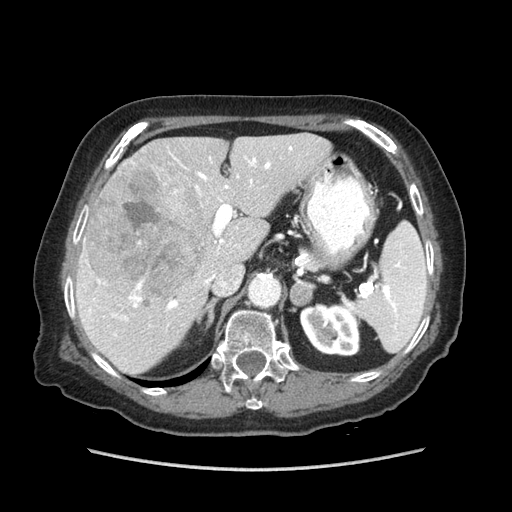
Contrast-enhanced abdominal CT (liver protocol), one axial slice. Slice 49 of 89 in the series (ordered by position). Reconstruction kernel STANDARD. 140 kVp. Soft-tissue window (W 400 / L 40 HU). 2.5 mm slice thickness. 512 × 512 image matrix, field of view 360 × 360 mm. From the clinical record (not read from this slice): diagnosis: hepatocellular carcinoma (patient treated with transarterial chemoembolisation; whether this scan precedes or follows treatment is not stated here); TNM stage (as recorded): Stage-IIIA; Child-Pugh class: A; tumour nodularity: multinodular; tumour size: 11 cm.
Structures marked on this image (semi-automatic segmentation, software-assisted and operator-edited):
- liver parenchyma outside the tumour (the mass and vessels are separate outlines, so this box may not span the whole liver): bounding box <76,134,330,374> (left, top, right, bottom; pixels)
- mass: <84,159,207,298>
- liver vessels: <89,146,293,320>